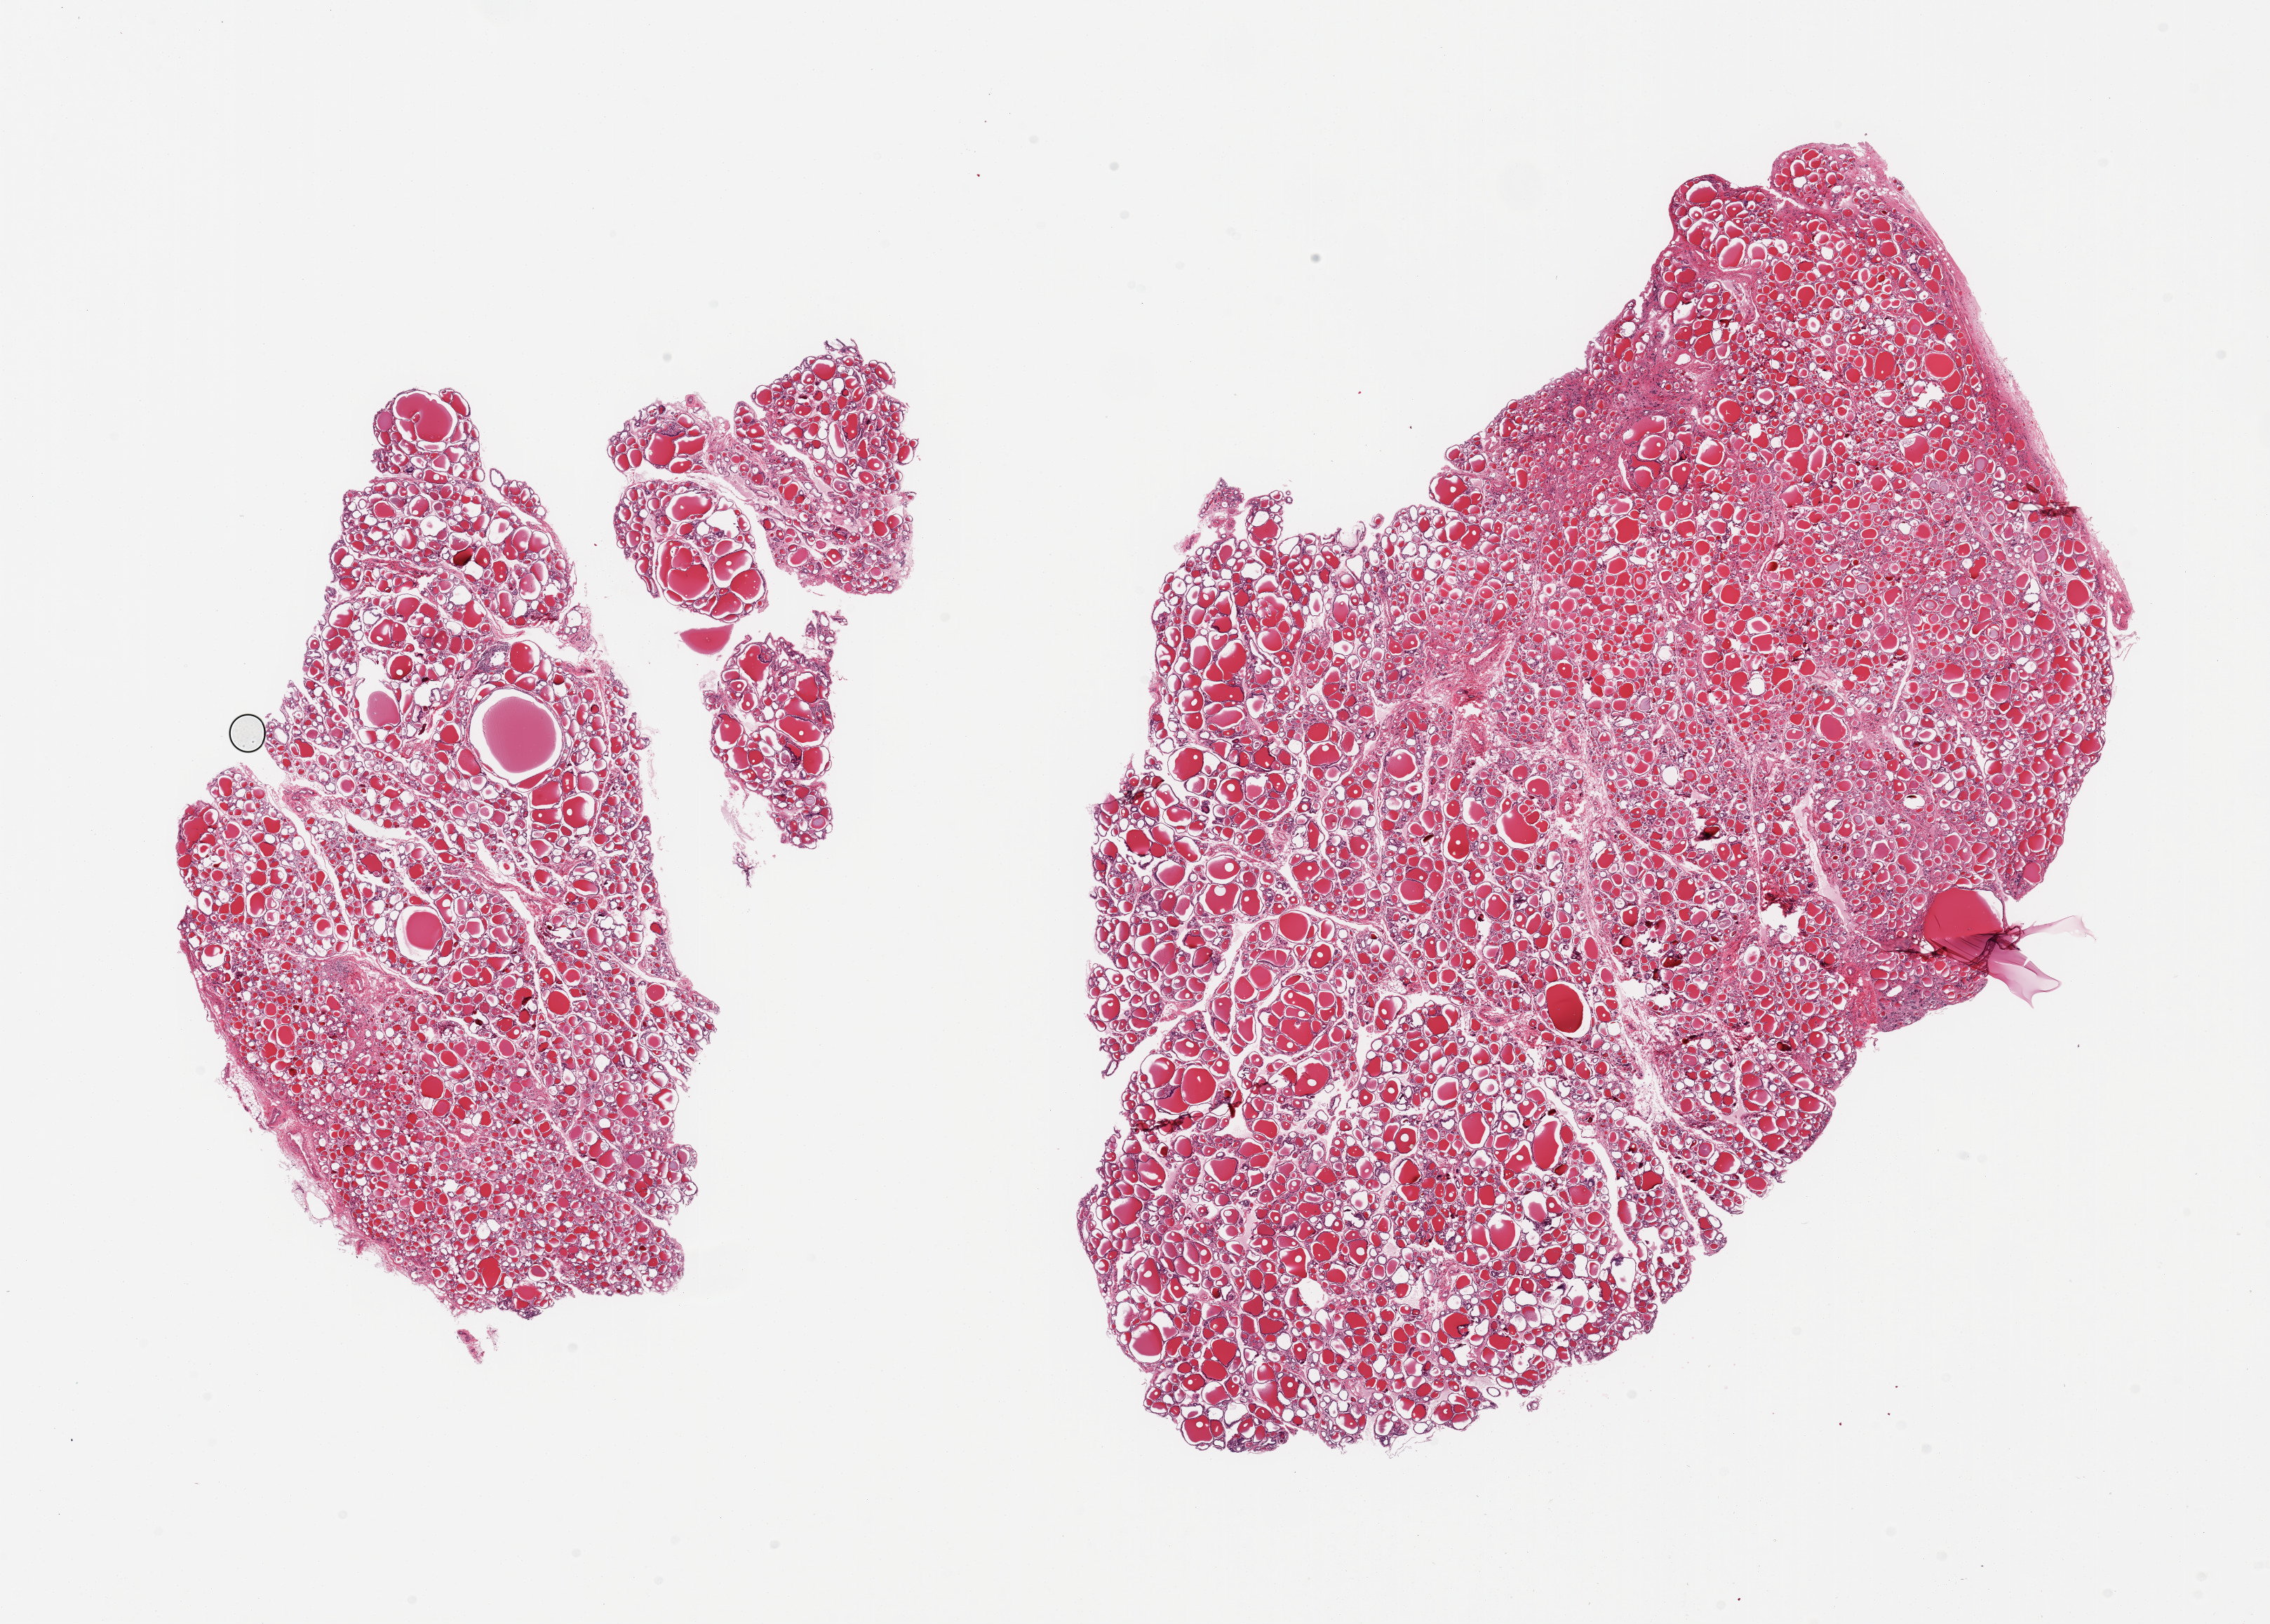
Whole-slide image, H&E stain, shown as a low-resolution overview of the whole scanned area (about 25.6 x 18.3 mm, from a 20x scan). PAXgene-fixed, paraffin-embedded tissue. Target tissue: thyroid. Tissue donor sample. Donor: female.
Review note (as recorded): 2 pieces; 1% fibrosis.